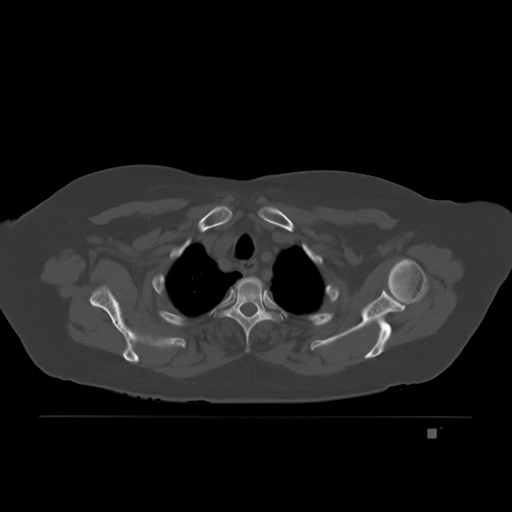
CT including the spine, one axial slice; slice 167 of 221 in the series (ordered by position); bone window (W 1800 / L 400 HU); 3 mm slice thickness; 512 × 512 image matrix. Female patient, age 63 years. From the clinical record (not read from this slice): primary cancer: breast.
Outlined on this slice (semi-automatic segmentation, software-assisted and operator-edited):
- T3 vertebra: bounding box (x1, y1, x2, y2) in pixels: (223, 298, 283, 325)